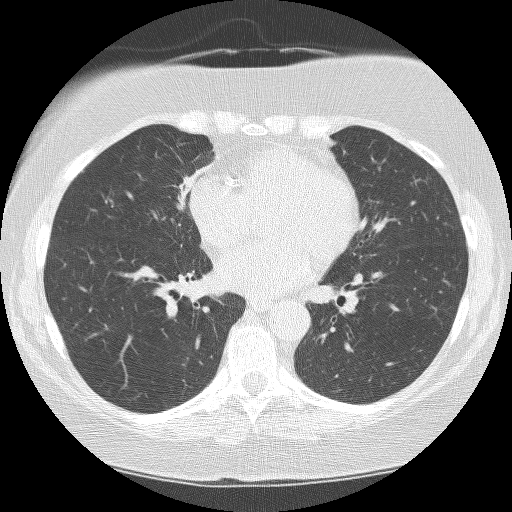
Low-dose screening chest CT, one axial slice; position 80 of 159 along the scan axis; reconstruction kernel BONE; 120 kVp; lung window (W 1500 / L -600 HU); 512 × 512 image matrix.
Annotated regions visible in this slice (expert manual segmentation):
- lesion 1 (tumor, hilum of right lung): bounding box [x1, y1, x2, y2] px = [178, 166, 210, 210]